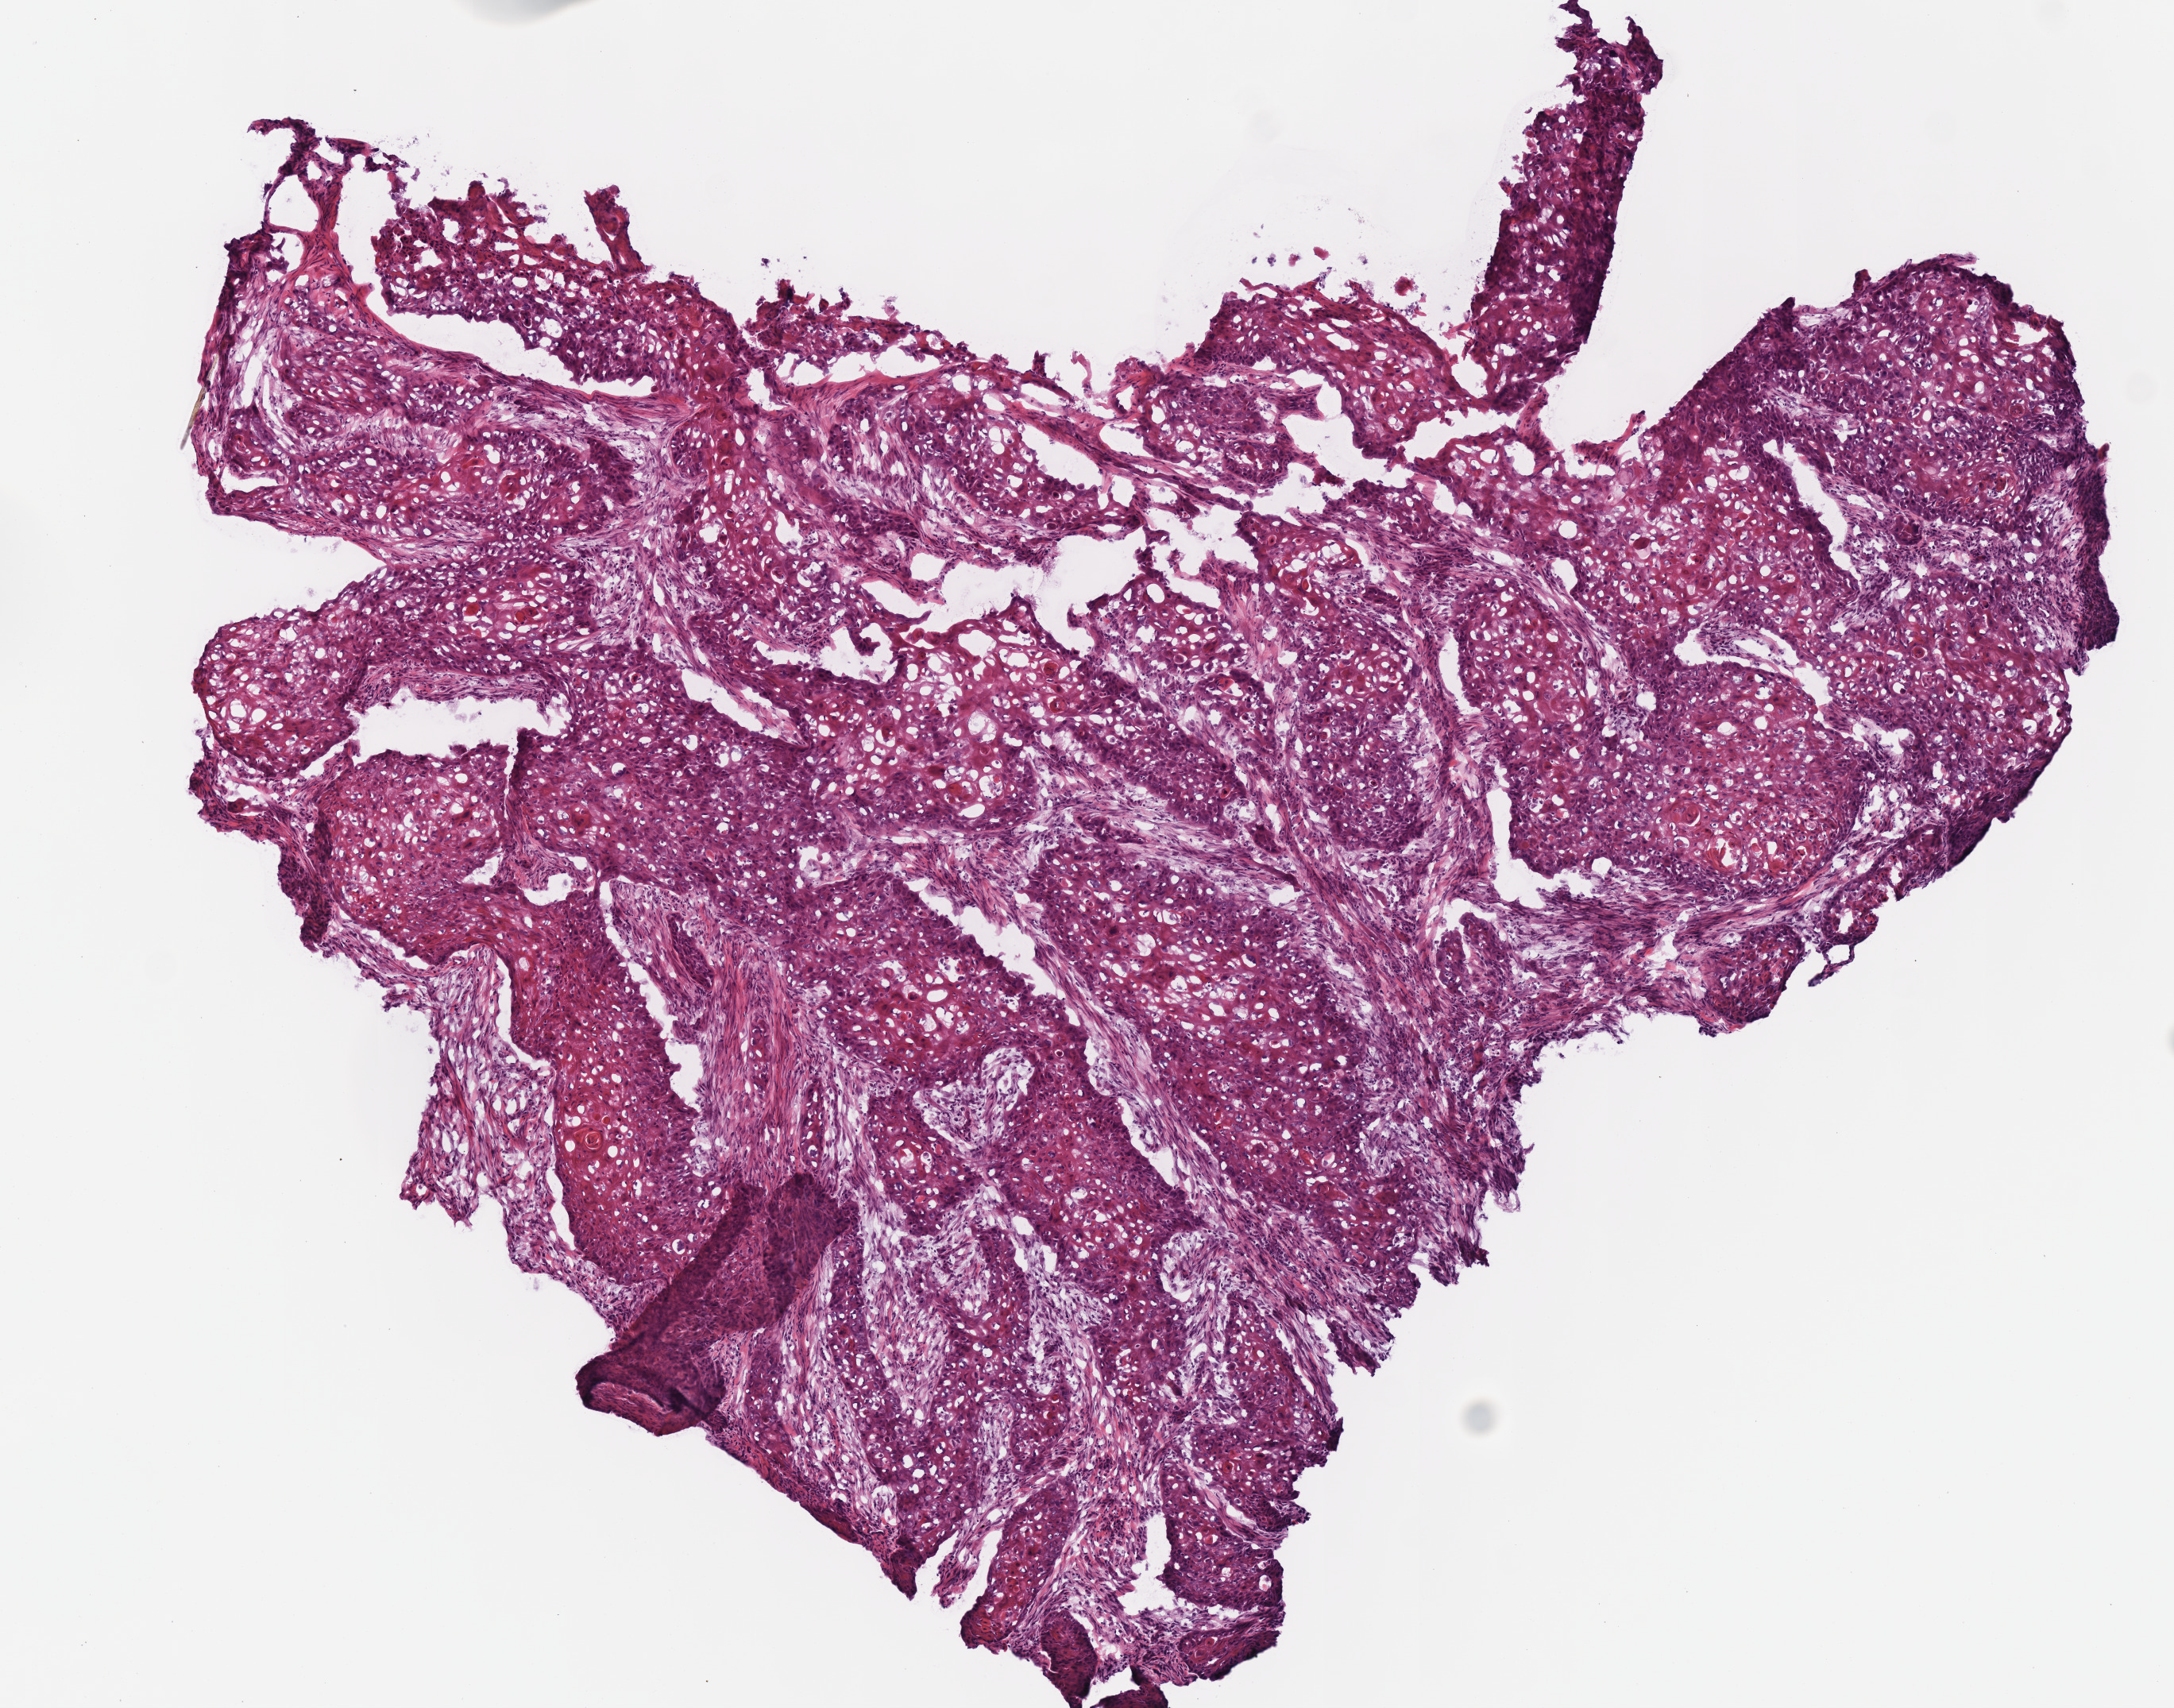
Digitized H&E-stained tissue section (whole slide), shown as a low-resolution overview of the whole scanned area (about 5.4 x 4.2 mm, from a 40x scan). Frozen section. Primary tumour sample from the head and neck. Male patient; age at initial diagnosis 79 years. Histologic grade: G1 (well differentiated). Pathologist review of this section (percent, as recorded): tumour cells 85%, tumour nuclei 80%, normal cells 0%, stromal cells 15%, necrosis 0%.
Diagnosis: Squamous cell carcinoma, NOS. TNM: T2 N0. AJCC pathologic stage: II (7th edition).